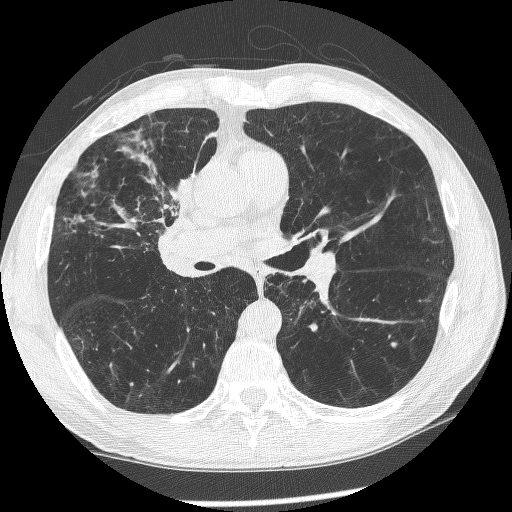
Low-dose screening chest CT, axial slice. Baseline screening round. Lung window (W 1500 / L -600 HU). 1.25 mm slice thickness. Lung (sharp) reconstruction kernel (BONE). 120 kVp. Slice 134 of 266 in the series. 512 × 512 image matrix. Male participant, aged 60 years at enrolment. Current smoker at enrolment.
Expert-annotated lung lesion, bounding box (x1, y1, x2, y2) in pixels: (146, 174, 215, 268). Screening reader's record for this exam (one nodule recorded; not confirmed to be the boxed lesion): non-calcified nodule or mass ≥4 mm, right upper lobe, 12 × 8 mm, spiculated (stellate) margins, mixed attenuation. Official screen result: positive, change unspecified: nodule(s) >= 4 mm or enlarging nodule(s), mass(es), or other non-specific abnormalities suspicious for lung cancer. Participant outcome: lung cancer diagnosed 208 days after this screen — squamous cell carcinoma, NOS, right upper lobe, right middle lobe, right main stem bronchus, poorly differentiated (G3), stage IV (AJCC 6th edition).